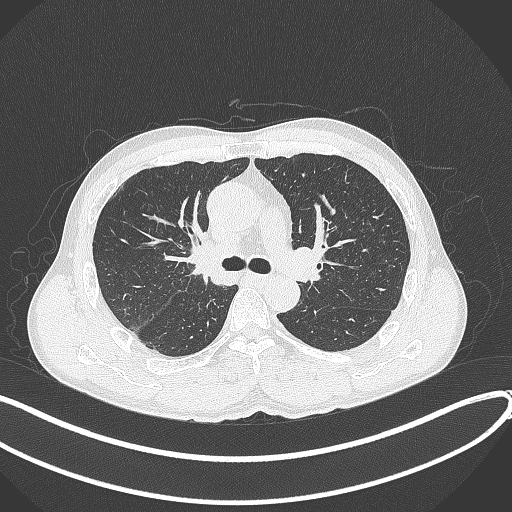
Chest CT, one axial slice; position 244 of 409 along the scan axis; reconstruction kernel B70f; lung window (W 1500 / L -600 HU); 512 × 512 image matrix, field of view 400 × 400 mm. Male patient, age 53 years. Case-level facts recorded for this patient, not image findings: clinical TNM (as recorded): T1b N0 M0.
Annotated regions visible in this slice (bounding box drawn by a radiologist):
- lung tumour (recorded histology: squamous cell carcinoma): bounding box [x1, y1, x2, y2] px = [184, 224, 227, 278]